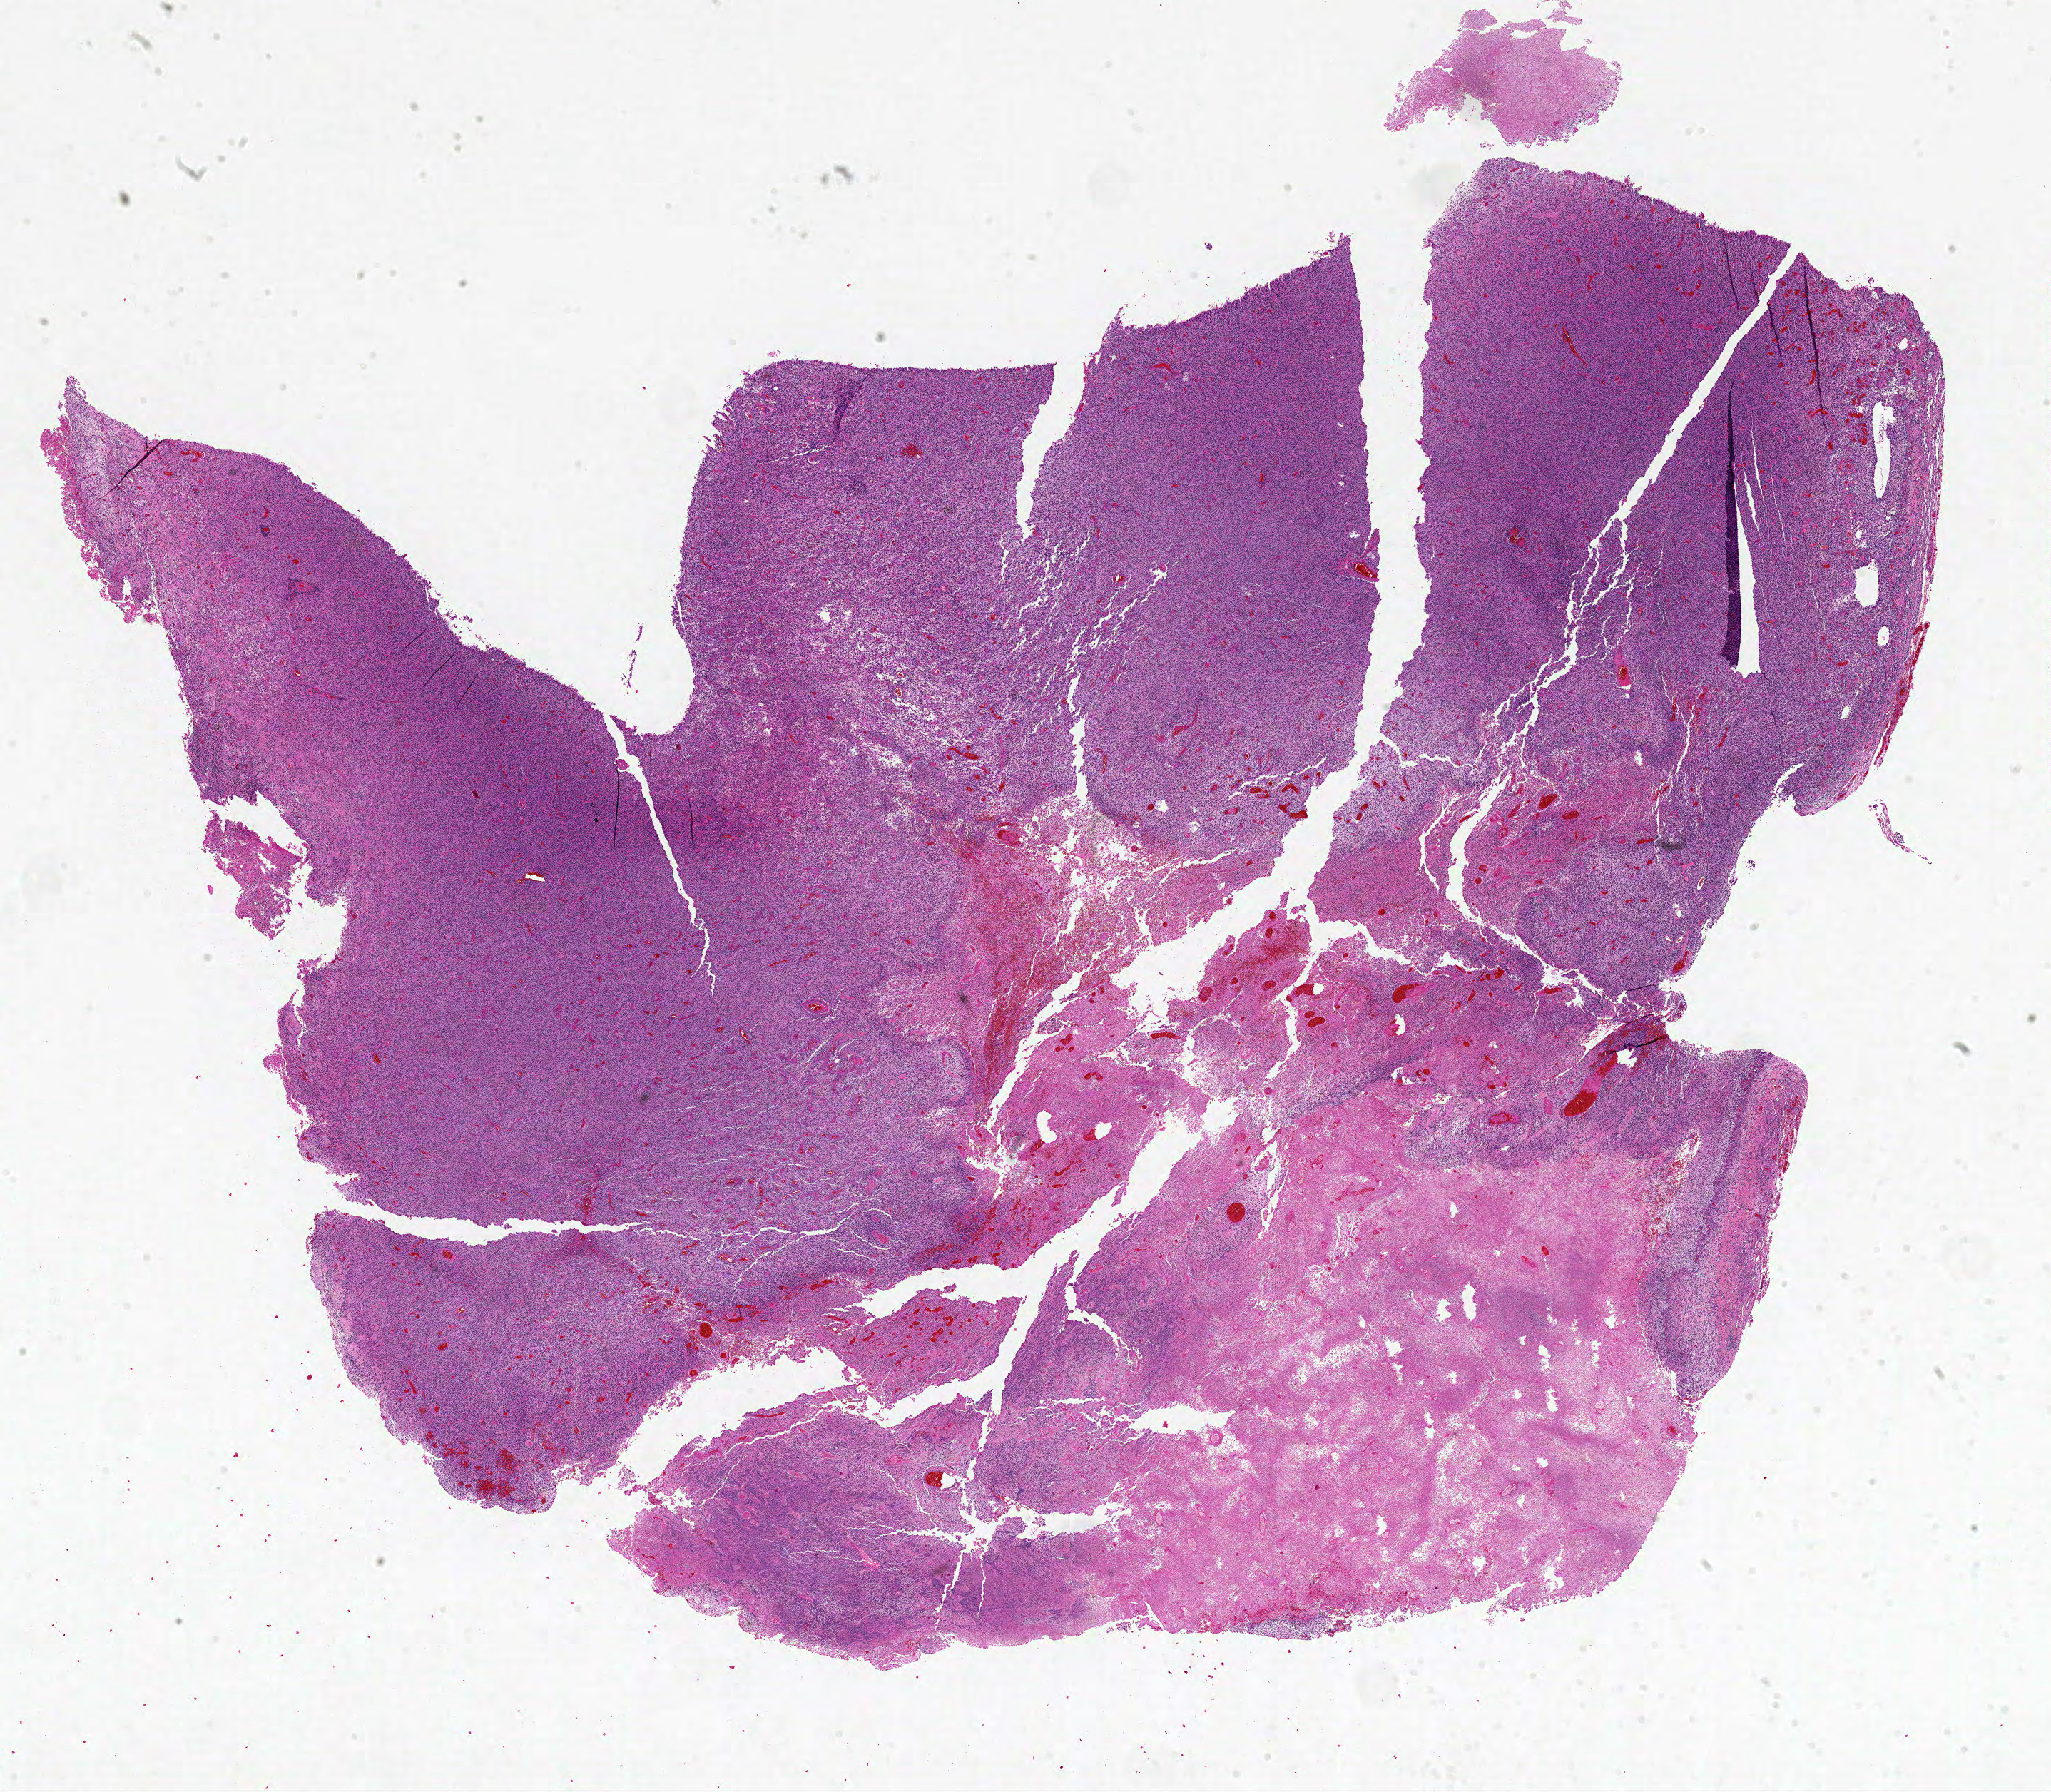
Hematoxylin and eosin (H&E) stained whole-slide image — a low-resolution overview of the entire scanned area, about 23.0 x 20.1 mm (acquisition: 20x scan); formalin-fixed paraffin-embedded (FFPE) diagnostic section; brain, primary tumour sample. Male, age 60 years at initial diagnosis.
Pathologic diagnosis: Glioblastoma.